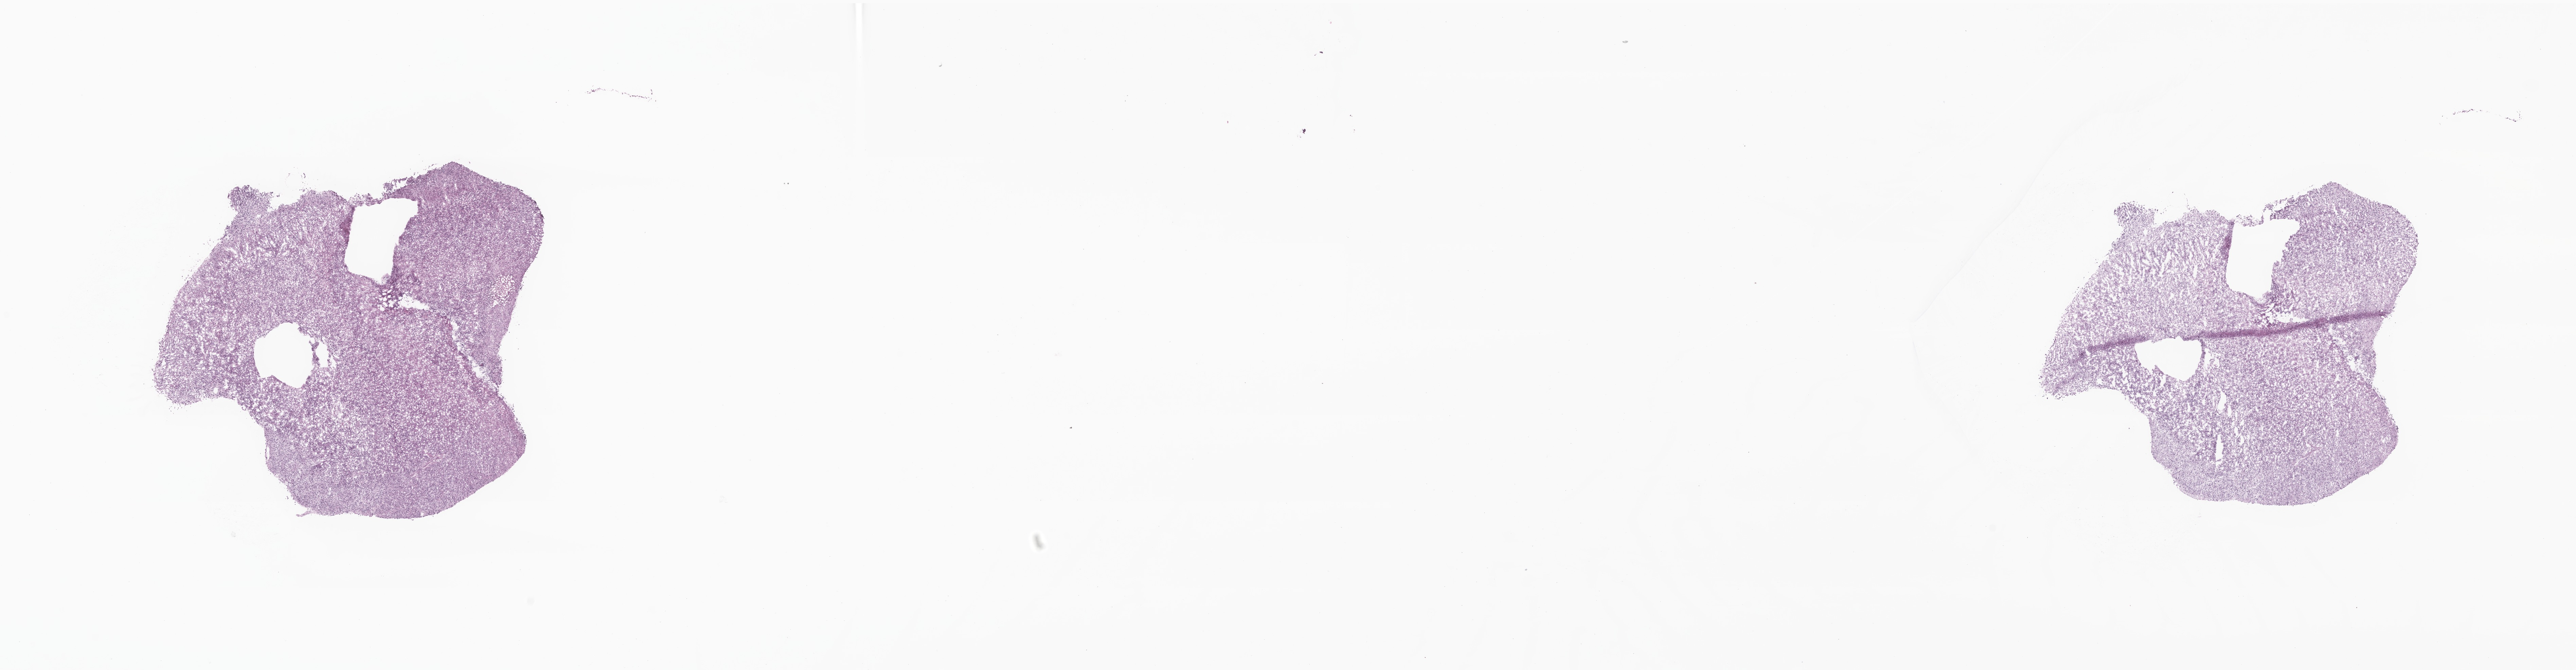
Whole-slide image, haematoxylin and eosin stain of tumor tissue from the cerebellum, low-resolution overview of the scanned area, about 32.0 x 8.3 mm; frozen section (OCT-embedded). Patient: male, age 103 months (8 years 7 months).
- diagnosis (ICD-O-3 morphology term): Medulloblastoma, NOS